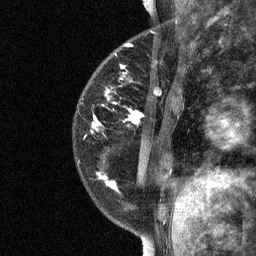
Breast MRI (dynamic contrast-enhanced), one sagittal slice. Dynamic contrast-enhanced study with each time point stored as its own series, time point 2 of 3 at this slice position (early post-contrast, ordered by acquisition time). 1.5 T. TE 4.8 ms, TR 27 ms. 2 mm slice thickness. 256 × 256 image matrix. Patient: female, 34 years. Case-level facts recorded for this patient, not image findings: setting: breast cancer imaged before/during neoadjuvant chemotherapy; receptor status: HR-positive, HER2-negative.
Outlined on this slice (semi-automatic segmentation, software-assisted and operator-edited):
- analysis volume of interest (the breast-tissue region the enhancement analysis was run in; not a lesion): bounding box (x1, y1, x2, y2) in pixels: (78, 44, 181, 191)
- tumour enhancement mask (voxels above the 90 % enhancement threshold inside the analysis volume of interest): (94, 90, 143, 188)